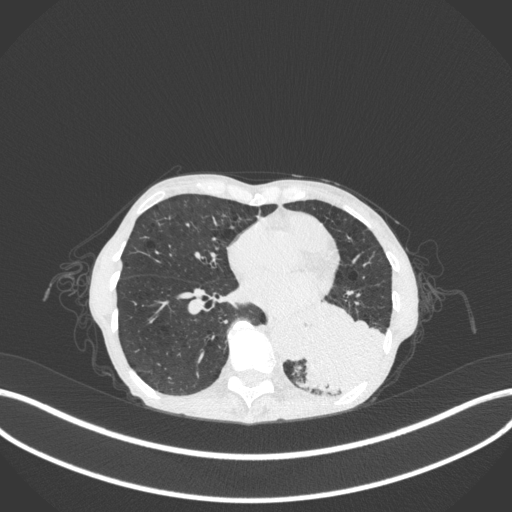
Chest CT, one axial slice; position 106 of 347 along the scan axis; reconstruction kernel B31f; 120 kVp; lung window (W 1500 / L -600 HU); 1 mm slice thickness; 512 × 512 image matrix. Patient: female, 70 years. From the clinical record (not read from this slice): clinical TNM (as recorded): T3 N0 M0.
Structures marked on this image (bounding box drawn by a radiologist):
- lung tumour (recorded histology: small cell carcinoma): box from (x=295, y=294) to (x=388, y=400) px